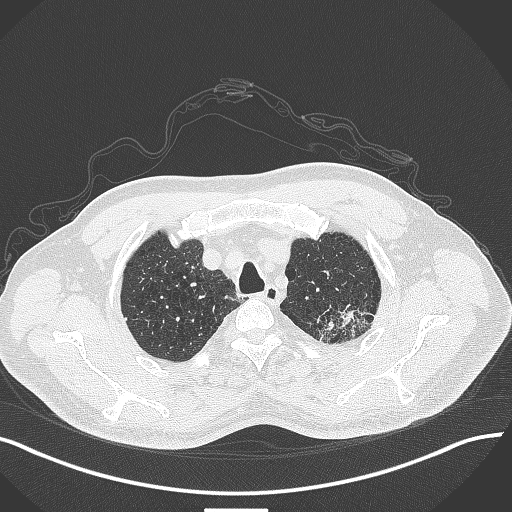
Chest CT, one axial slice; slice 360 of 429 in the series (ordered by position); reconstruction kernel B70f; 120 kVp; lung window (W 1500 / L -600 HU); 1 mm slice thickness; 512 × 512 image matrix, field of view 400 × 400 mm. Patient: male, 55 years. Case-level facts recorded for this patient, not image findings: clinical TNM (as recorded): T3 N0 M1c; histopathological grade: G3.
Structures marked on this image (rectangle marked by the reading radiologist):
- lung tumour (recorded histology: adenocarcinoma): box from (x=304, y=303) to (x=382, y=348) px